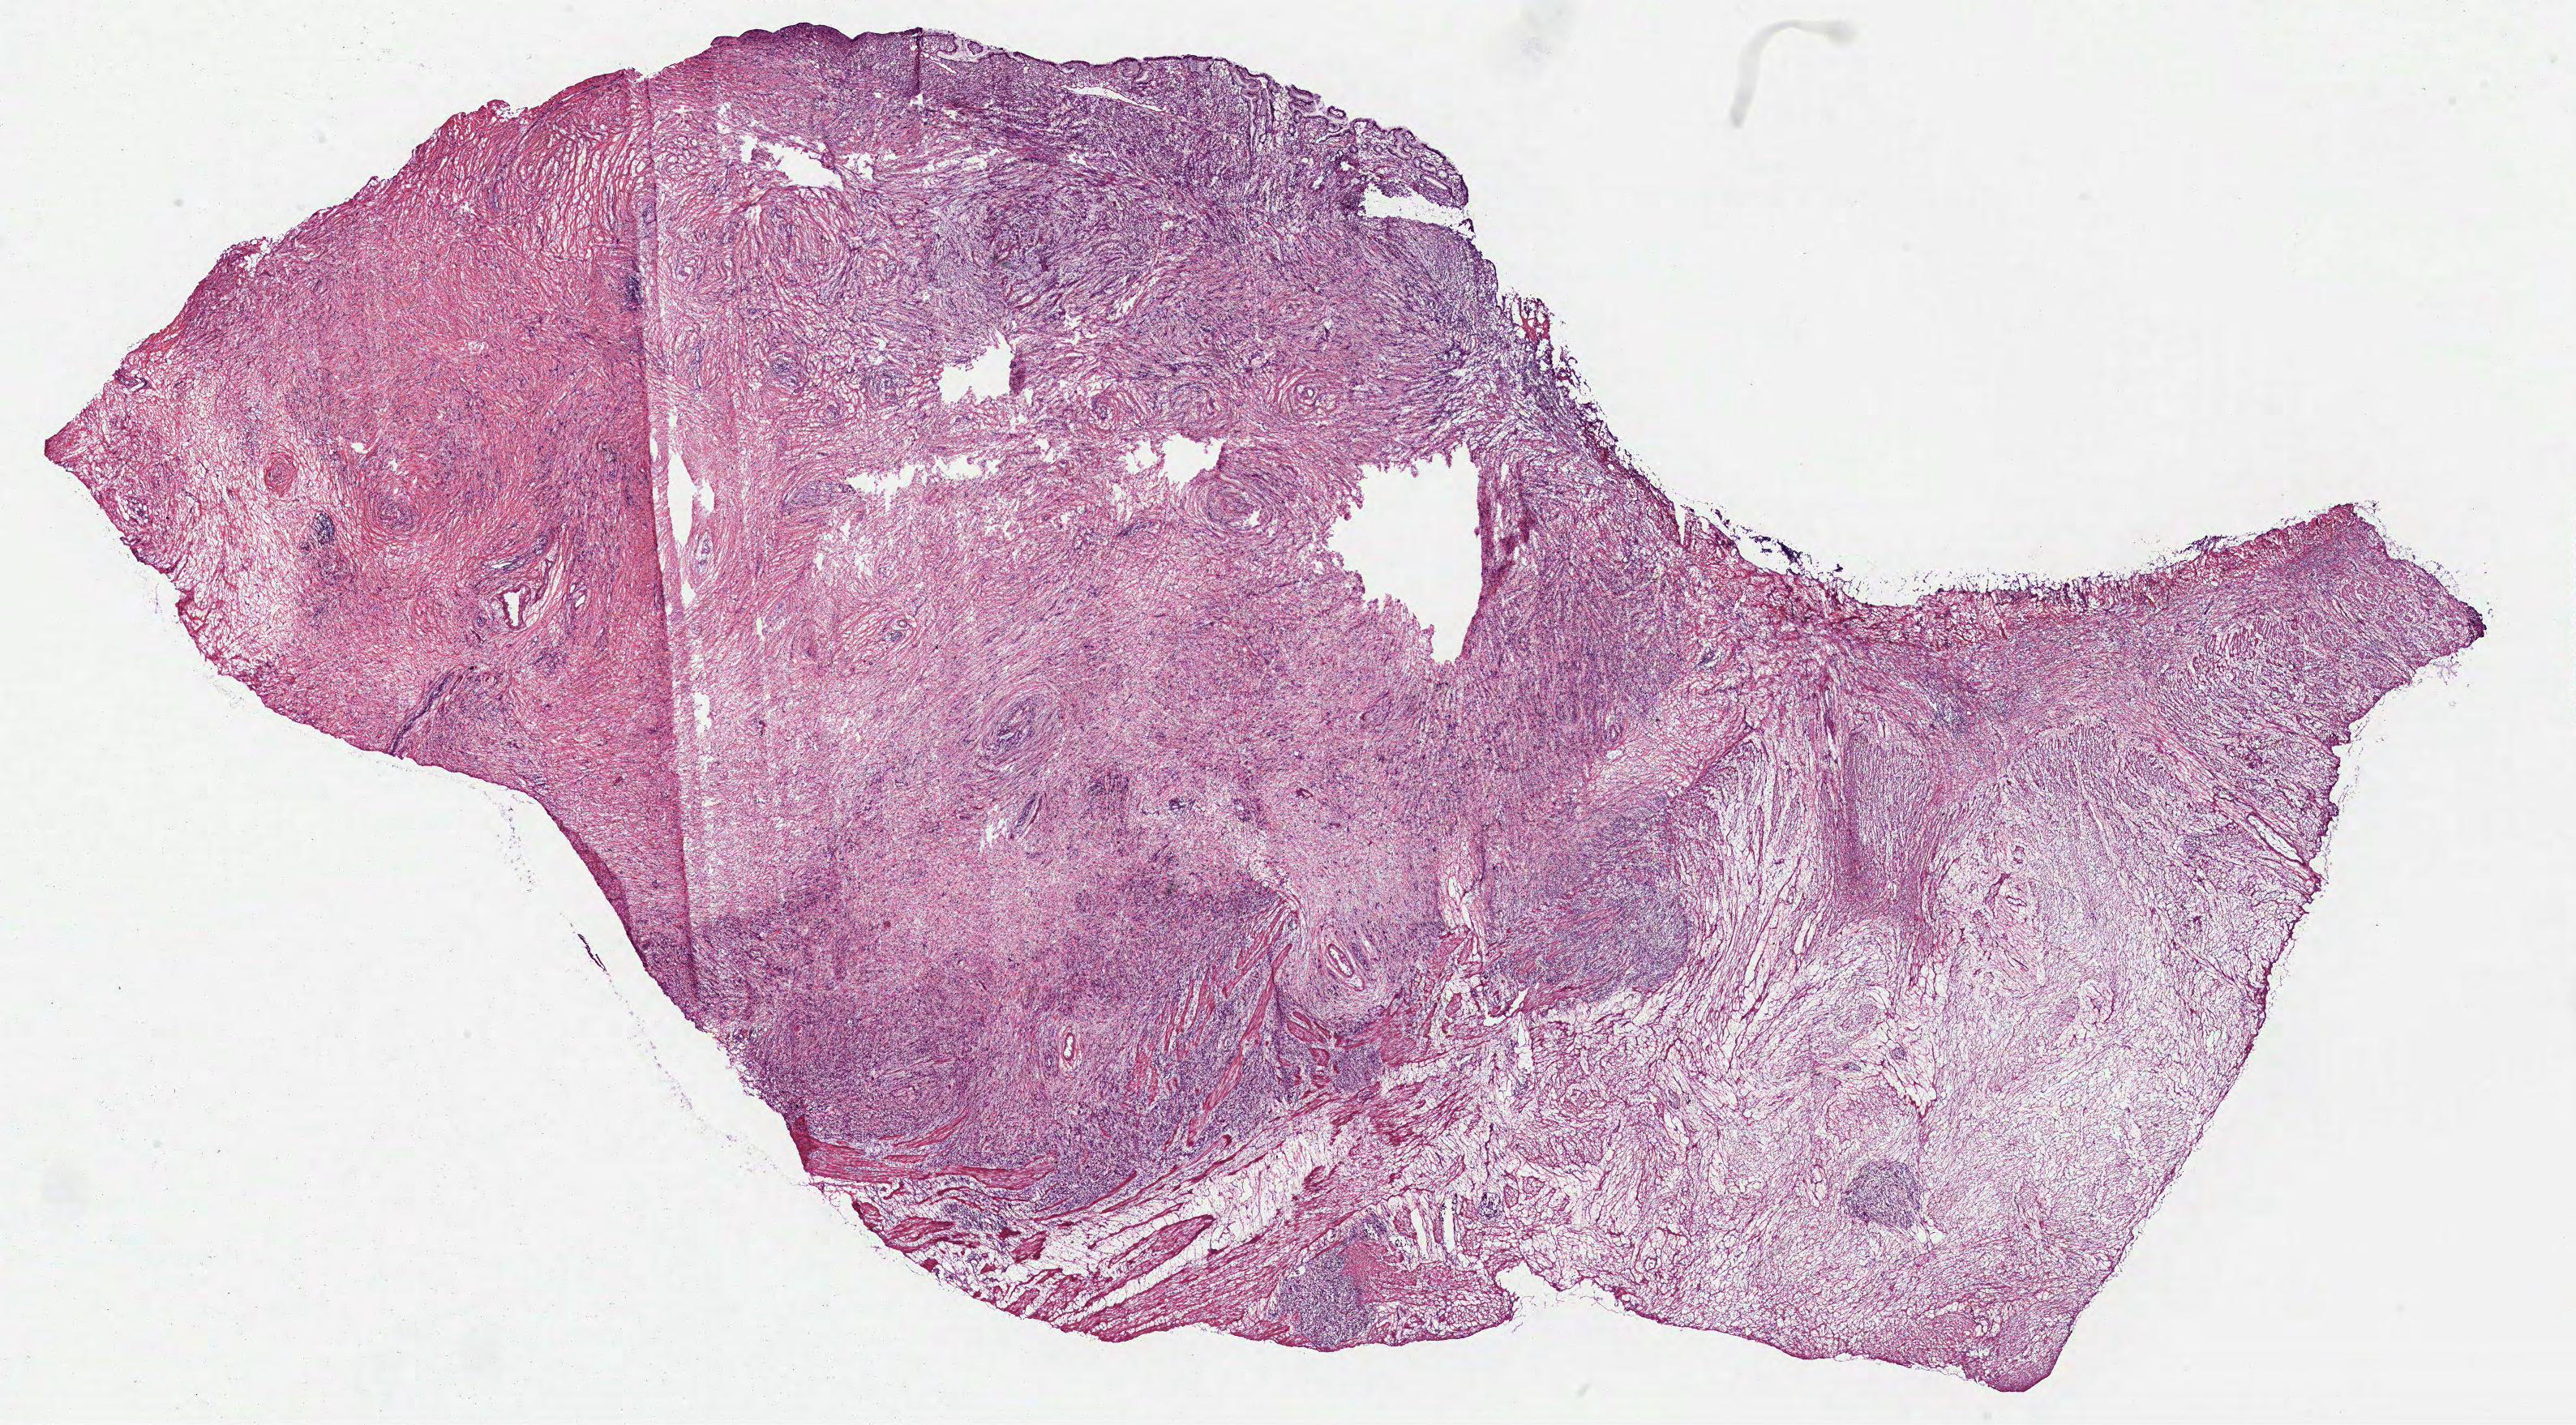
Digitized H&E tissue section (whole slide) — shown as a low-resolution overview of the whole scanned area (about 25.6 x 14.2 mm), frozen section, stomach, primary tumour sample. Female, age 50 years at initial diagnosis. Histologic grade: GX (grade cannot be assessed). Pathologist review of this section (percent, as recorded): tumour cells 45%, tumour nuclei 60%, normal cells 5%, stromal cells 50%, necrosis 0%.
- AJCC pathologic stage: IV (7th edition)
- histologic diagnosis: Adenocarcinoma, intestinal type (body of stomach)
- lymph nodes positive (case pathology): 7 of 8 examined